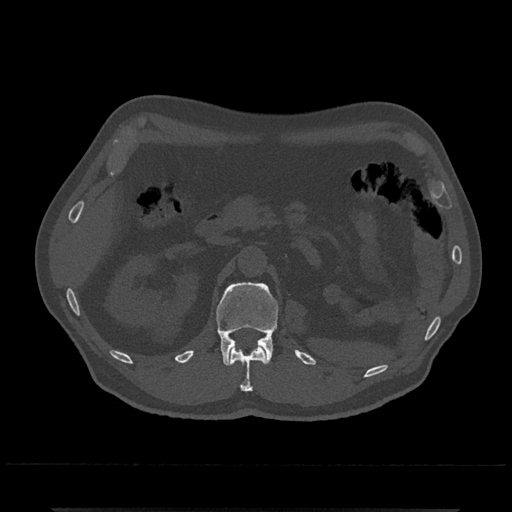
CT including the spine, one axial slice. Slice 385 of 797 in the series (ordered by position). Reconstruction kernel Br40s/3. 120 kVp. Bone window (W 1800 / L 400 HU). 0.5 mm slice thickness. 512 × 512 image matrix, field of view 393 × 393 mm. Male patient, age 67 years. From the clinical record (not read from this slice): primary cancer: prostate.
Structures marked on this image (semi-automatic segmentation, software-assisted and operator-edited):
- L1 vertebra: bounding box [x1, y1, x2, y2] px = [216, 282, 278, 366]
- T12 vertebra: [230, 346, 267, 392]